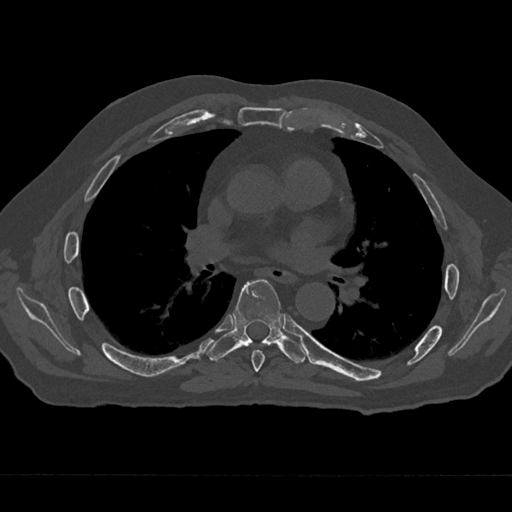
CT including the spine, one axial slice; position 390 of 797 along the scan axis; reconstruction kernel Br40s/3; bone window (W 1800 / L 400 HU); 0.5 mm slice thickness; 512 × 512 image matrix, field of view 377 × 377 mm. Patient: male, 75 years. From the clinical record (not read from this slice): primary cancer: renal.
Outlined on this slice (semi-automatic segmentation, software-assisted and operator-edited):
- T6 vertebra: bounding box <251,350,265,372> (left, top, right, bottom; pixels)
- T7 vertebra: <207,279,305,363>